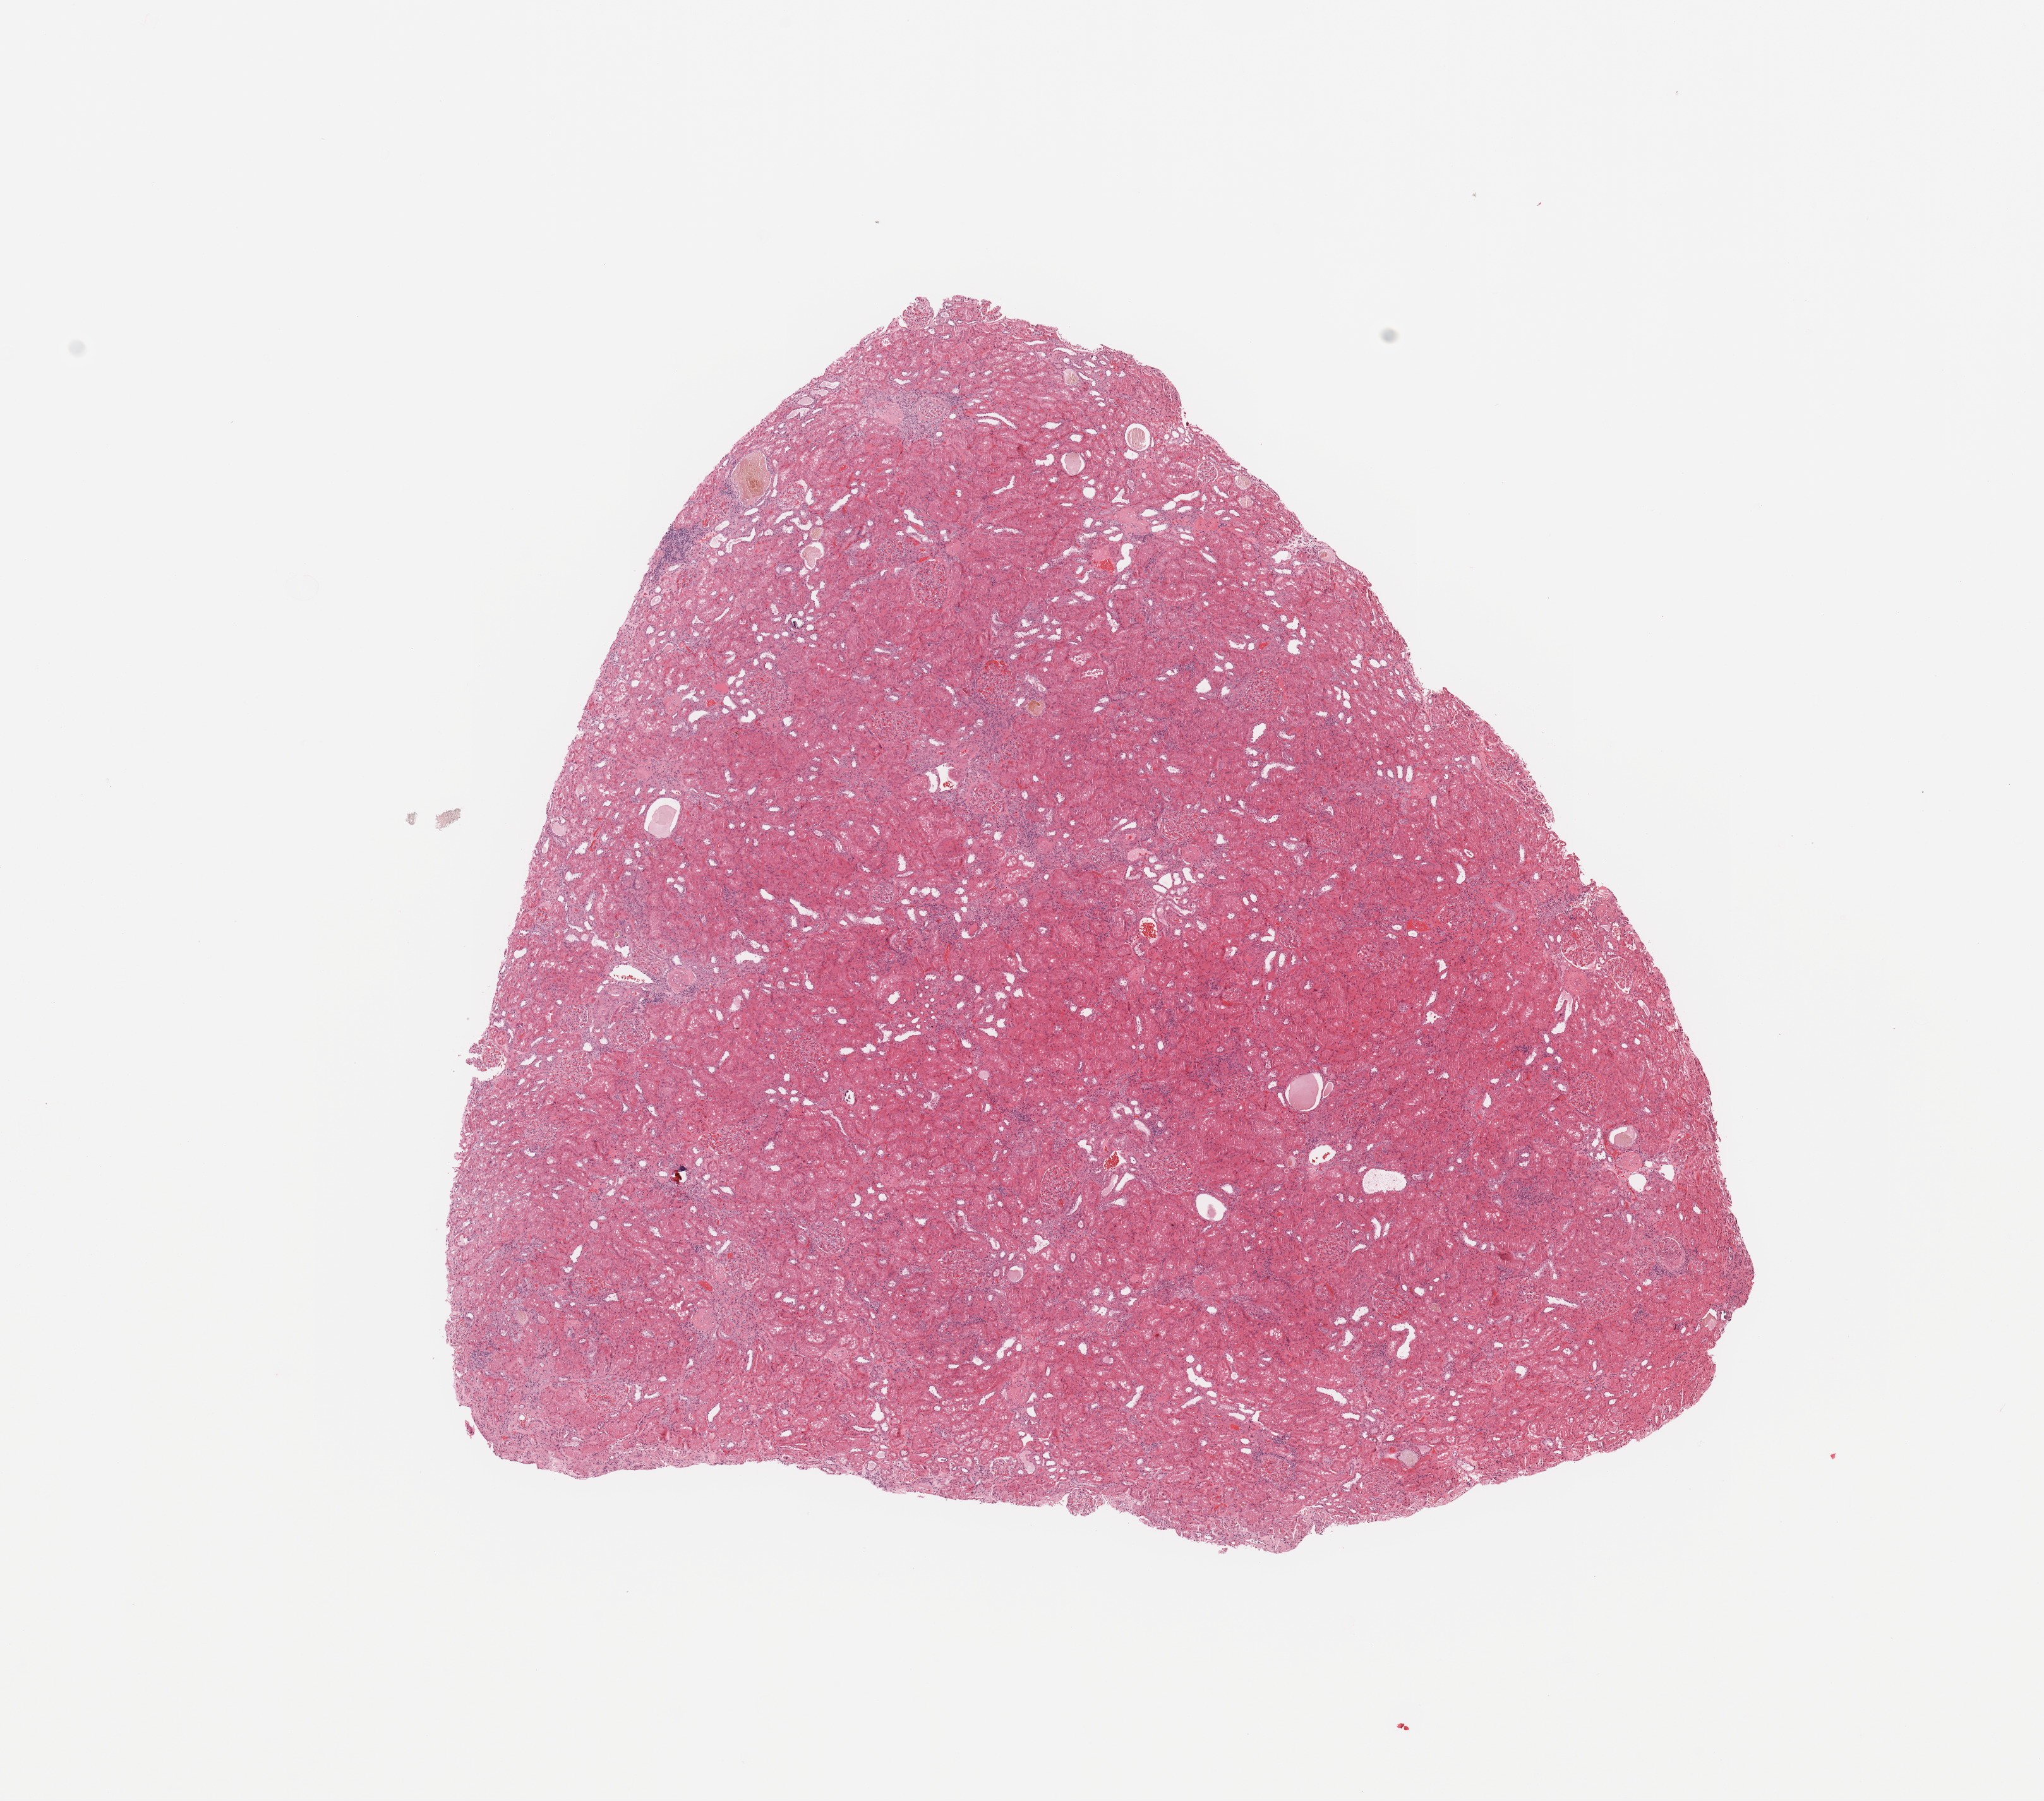
Digitized H&E-stained tissue section (whole slide) — low-resolution overview of the scanned area, about 12.8 x 11.3 mm (slide scanned at 20x), normal (non-tumour) tissue sample, sampled site: kidney. 68-year-old female patient.
* this section: normal (non-tumour) tissue from the same patient
* patient diagnosis: Renal cell carcinoma, NOS